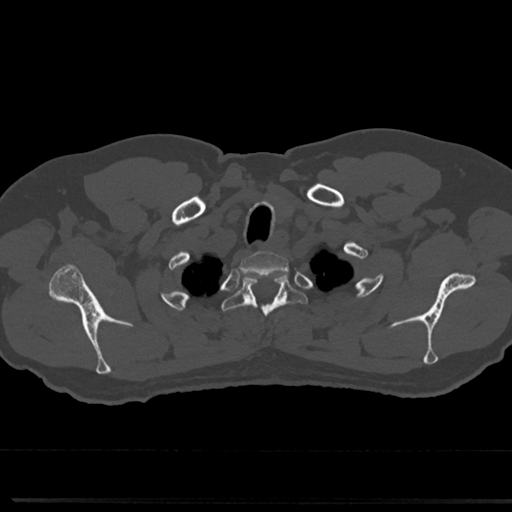
CT including the spine, one axial slice; position 645 of 817 along the scan axis; 120 kVp; bone window (W 1800 / L 400 HU); 0.5 mm slice thickness; 512 × 512 image matrix, field of view 355 × 355 mm. Patient: male, 61 years. From the clinical record (not read from this slice): primary cancer: prostate.
Structures marked on this image (semi-automatic segmentation, software-assisted and operator-edited):
- T1 vertebra: box from (x=243, y=252) to (x=286, y=266) px
- T2 vertebra: (x=226, y=273)–(x=304, y=328)